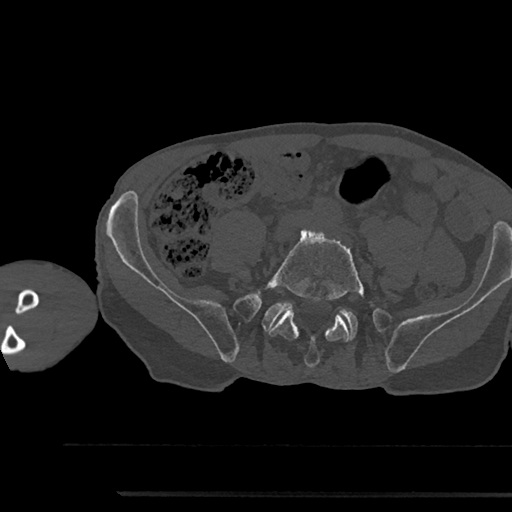
CT including the spine, one axial slice; reconstruction kernel Br40s/3; 120 kVp; bone window (W 1800 / L 400 HU); 0.5 mm slice thickness; 512 × 512 image matrix, field of view 367 × 367 mm. Male patient, age 79 years. Case-level facts recorded for this patient, not image findings: primary cancer: prostate.
Annotated regions visible in this slice (semi-automatically segmented with operator editing):
- L5 vertebra: bounding box <263,229,364,368> (left, top, right, bottom; pixels)